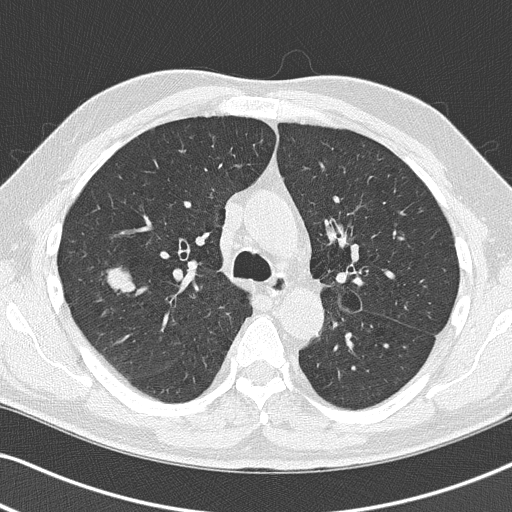
Axial slice from a low-dose chest CT screening exam; baseline annual screen; lung window (W 1500 / L -600 HU); 2 mm slice thickness; lung (sharp) reconstruction kernel (B50f); 120 kVp. Male, age 67 years at enrolment.
Lesion marked by an expert reader, box from (x=74, y=256) to (x=150, y=315) px. The exam's reader record, not a measurement of the box and not confirmed to be the same lesion: non-calcified nodule or mass ≥4 mm, right upper lobe, 26 × 24 mm, spiculated (stellate) margins, soft tissue attenuation. Official screen result: positive, change unspecified: nodule(s) >= 4 mm or enlarging nodule(s), mass(es), or other non-specific abnormalities suspicious for lung cancer.